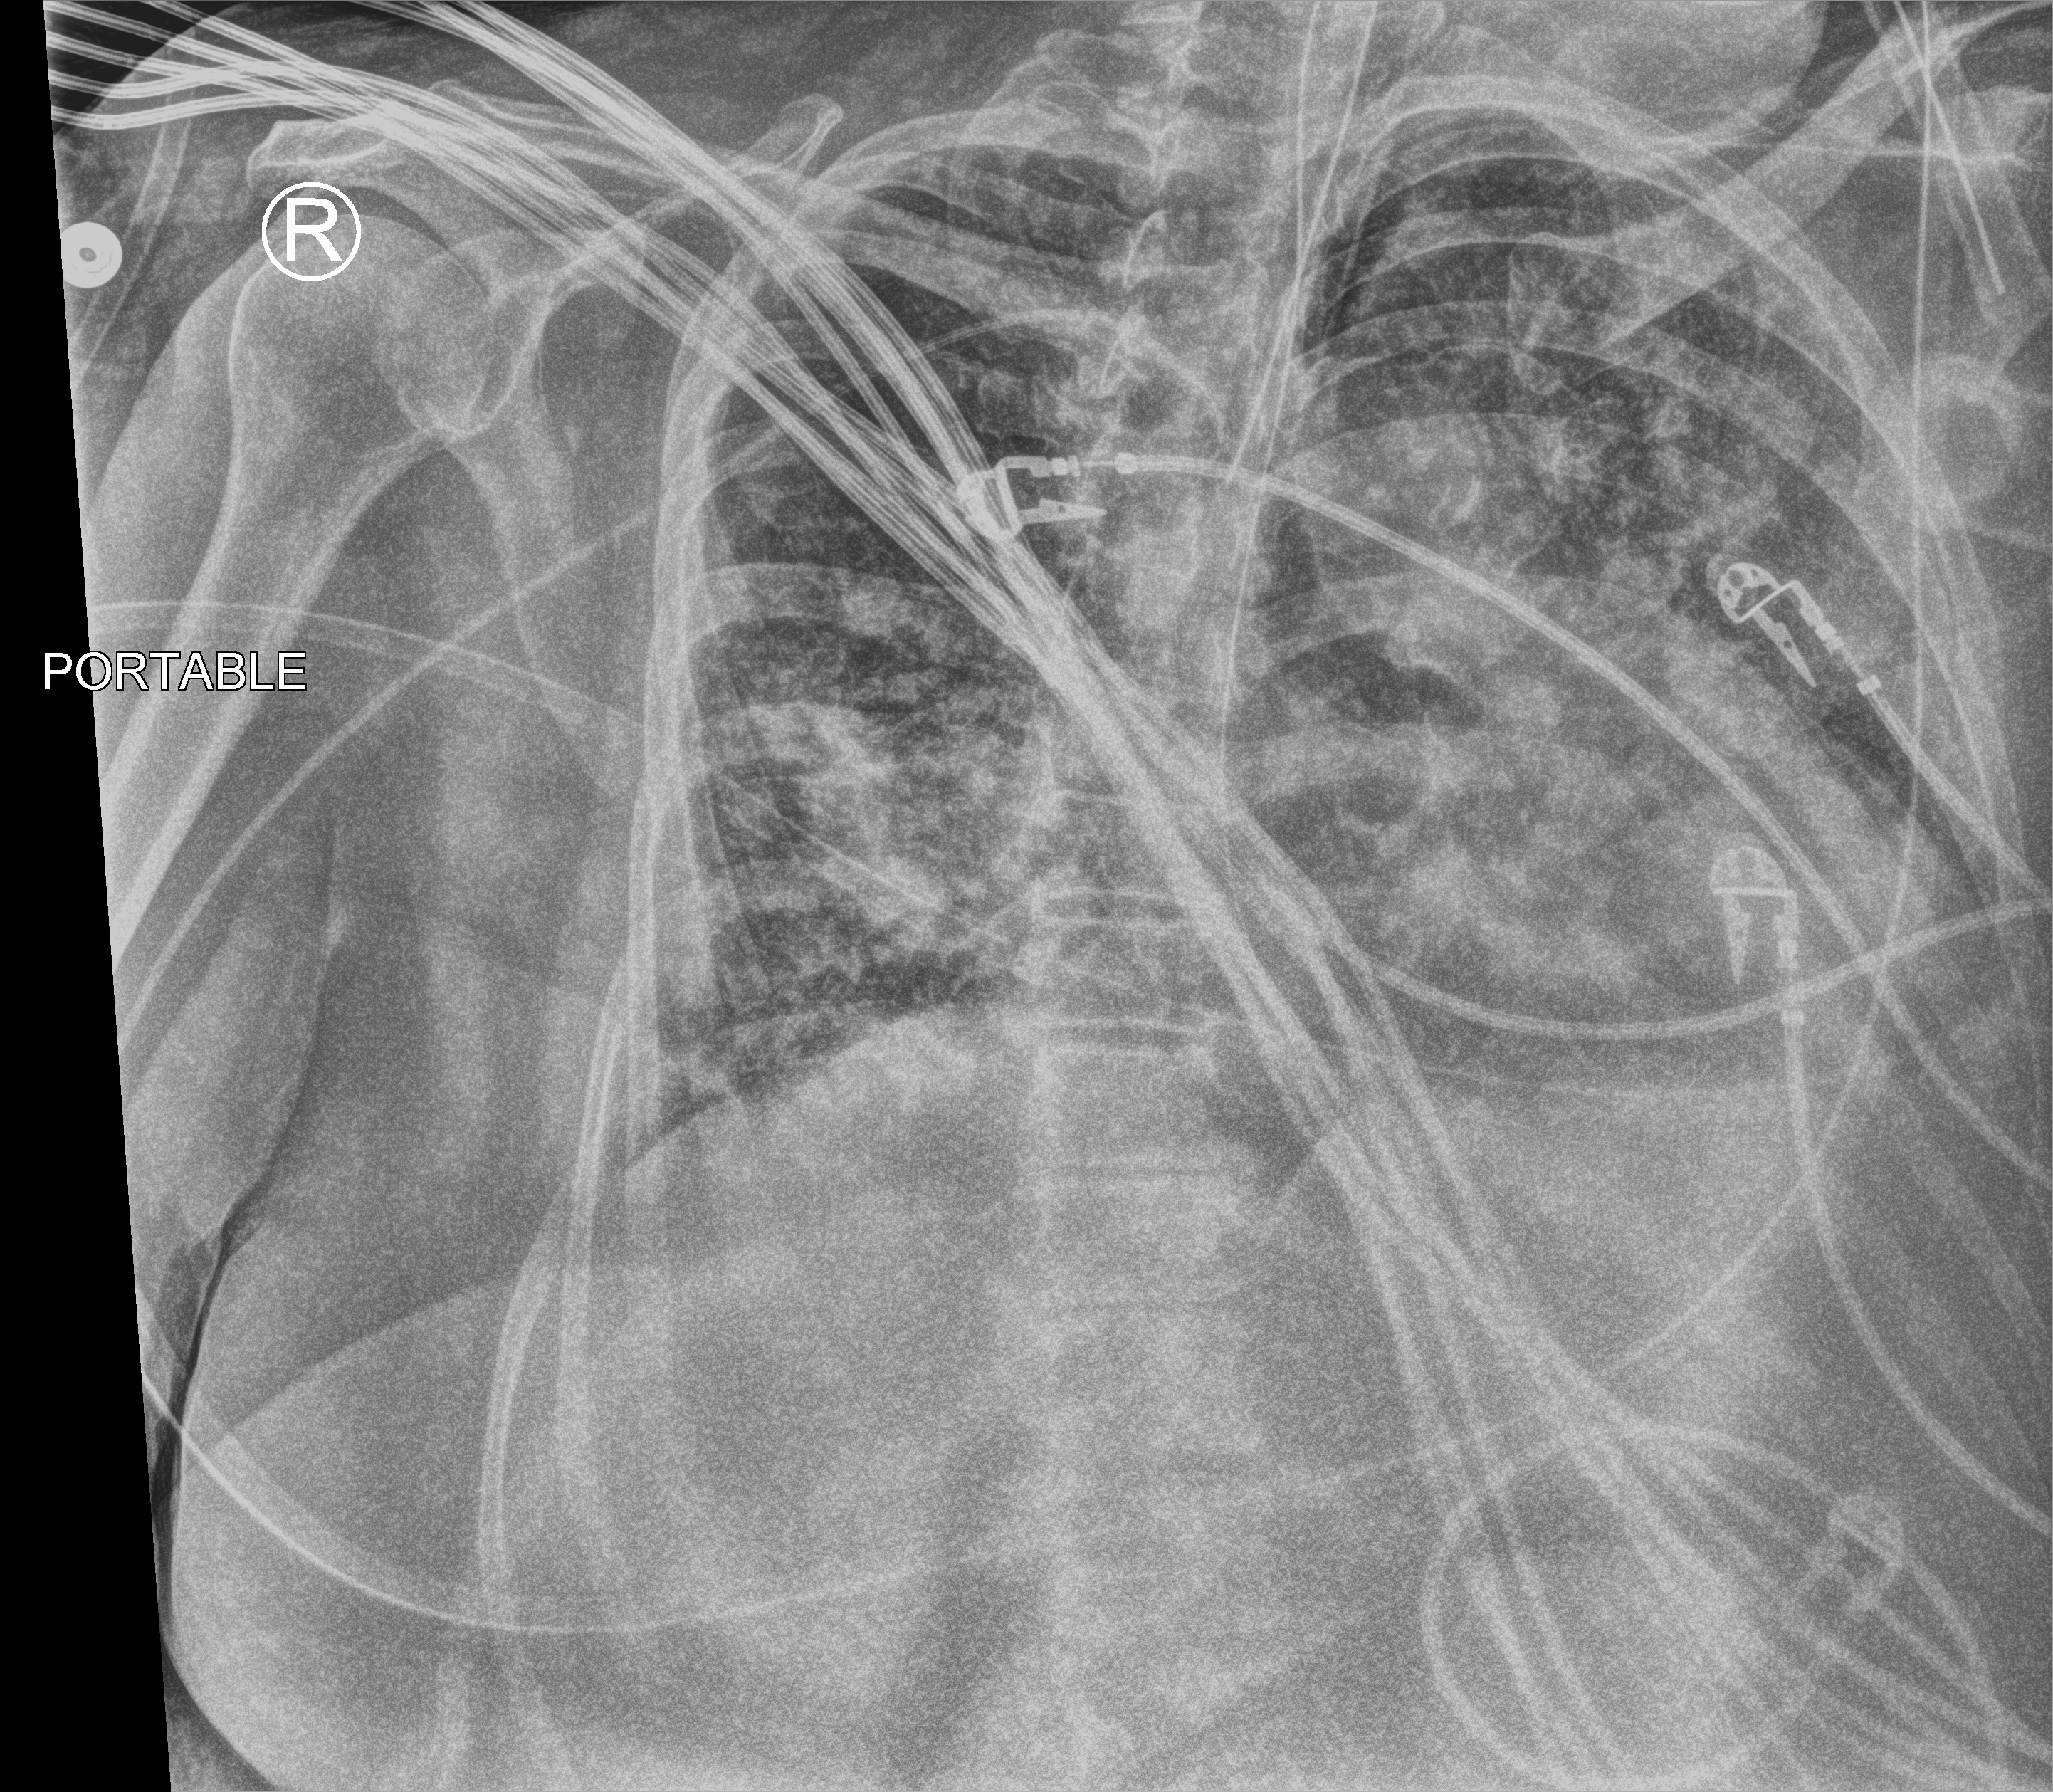
Bedside chest radiograph (computed radiography). Female patient hospitalised with COVID-19, age 60–74 years.
Hospital-stay facts (about this admission, not read from this image; timing relative to this image not recorded): smoking status (admission record): never.